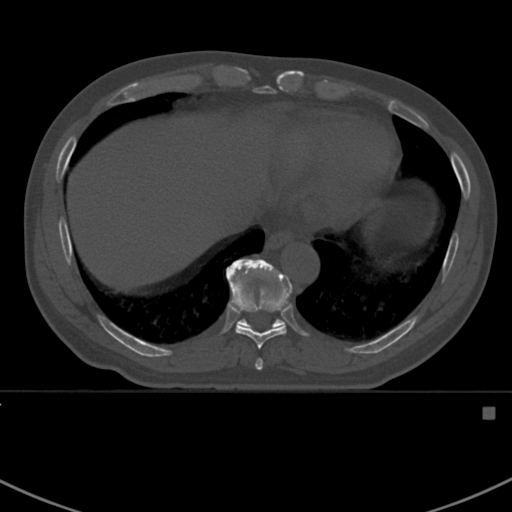
CT including the spine, one axial slice. Position 379 of 412 along the scan axis. Reconstruction kernel Br40s. 120 kVp. Bone window (W 1800 / L 400 HU). 512 × 512 image matrix, field of view 358 × 358 mm. Patient: male, 59 years. From the clinical record (not read from this slice): primary cancer: prostate.
Structures marked on this image (semi-automatic segmentation, software-assisted and operator-edited):
- T10 vertebra: bounding box <226,258,293,328> (left, top, right, bottom; pixels)
- T8 vertebra: <255,358,263,370>
- T9 vertebra: <228,286,288,350>